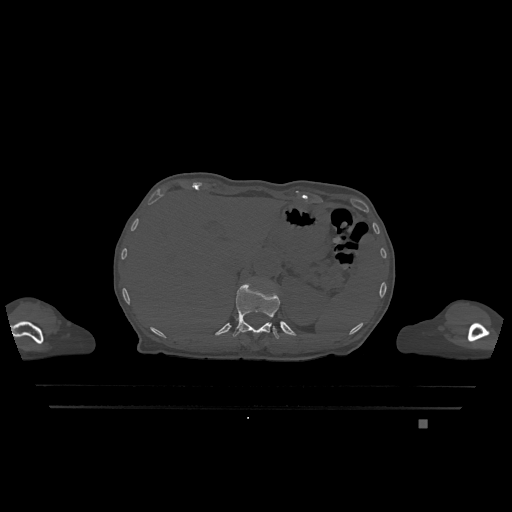
CT including the spine, one axial slice; position 531 of 1317 along the scan axis; bone window (W 1800 / L 400 HU); 0.5 mm slice thickness; 512 × 512 image matrix, field of view 500 × 500 mm. Patient: female, 74 years. Case-level facts recorded for this patient, not image findings: primary cancer: lung; vertebrae with lytic lesions (as recorded): T1, T4, T5, T6, L4, L5.
Annotated regions visible in this slice (semi-automatic segmentation, software-assisted and operator-edited):
- T12 vertebra: box from (x=232, y=283) to (x=280, y=339) px